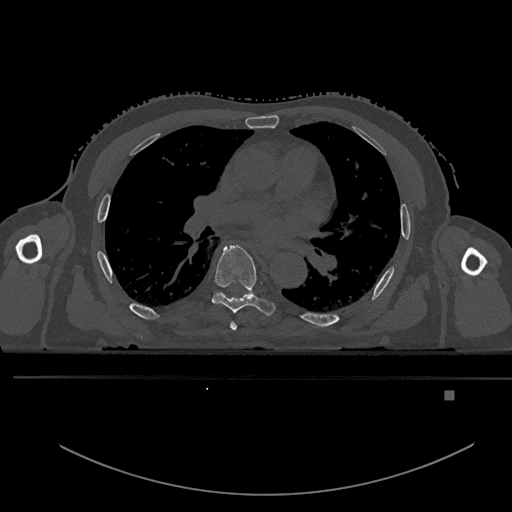
CT including the spine, one axial slice; bone window (W 1800 / L 400 HU); 0.5 mm slice thickness; 512 × 512 image matrix, field of view 456 × 456 mm. Male patient, age 82 years. From the clinical record (not read from this slice): primary cancer: prostate; vertebrae with lytic lesions (as recorded): T11, T9, T8, T2.
Annotated regions visible in this slice (semi-automatically segmented with operator editing):
- T5 vertebra: bounding box (x1, y1, x2, y2) in pixels: (230, 321, 237, 331)
- T6 vertebra: (212, 245, 275, 316)